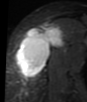
MRI of an extremity soft-tissue mass, one axial slice. Slice 29 of 48 in the series (ordered by position). STIR. MR volume resampled by the dataset authors to the PET/CT grid (not the native acquisition matrix). 3.27 mm slice thickness. 87 × 102 image matrix, field of view 85 × 100 mm. Female patient. From the clinical record (not read from this slice): histological type: synovial sarcoma; grade: intermediate; site of the primary tumour: right thigh.
Outlined on this slice (expert contour drawn on MRI and transferred to this co-registered scan by the dataset authors):
- gross tumour volume including surrounding oedema: bounding box <15,24,64,78> (left, top, right, bottom; pixels)
- gross tumour volume (mass): <17,24,64,76>